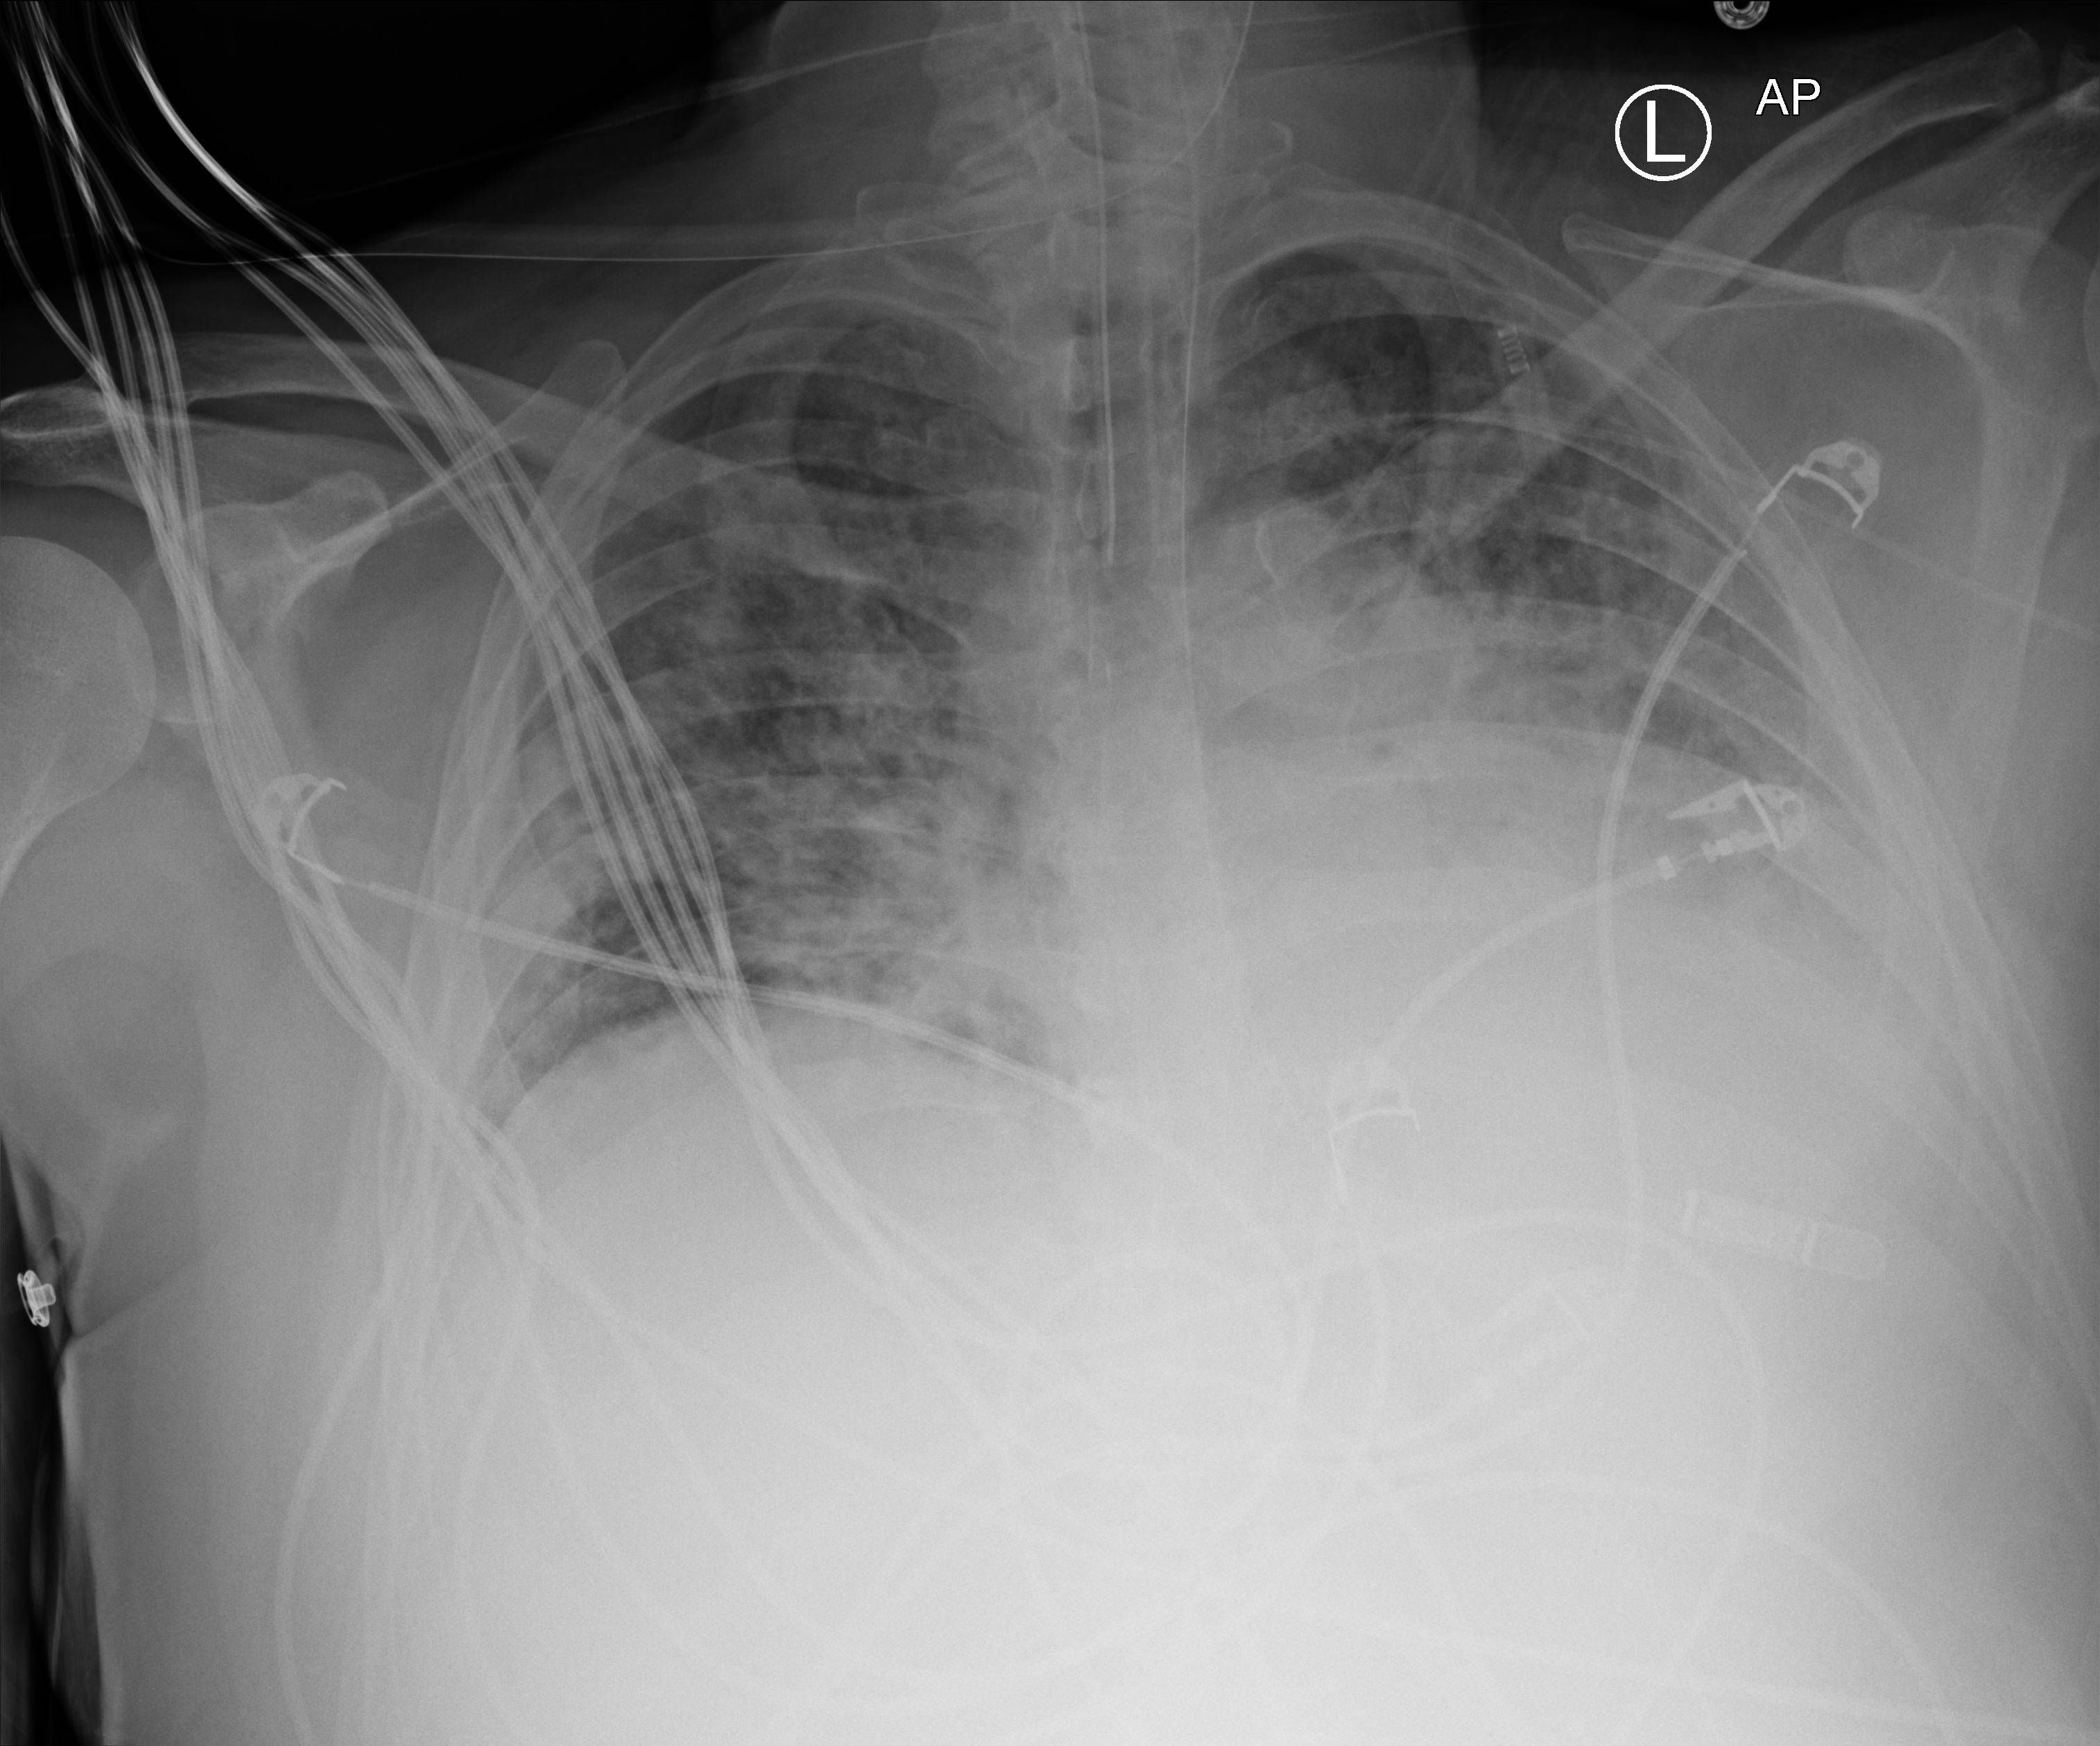
Chest X-ray (portable); anteroposterior (AP) projection. Male patient hospitalised with COVID-19, age 18–59 years.
From the hospital-stay record, not from the radiograph (when in the stay this image was taken is not recorded): mechanically ventilated during this hospital stay: yes; admitted to intensive care during this hospital stay: yes.